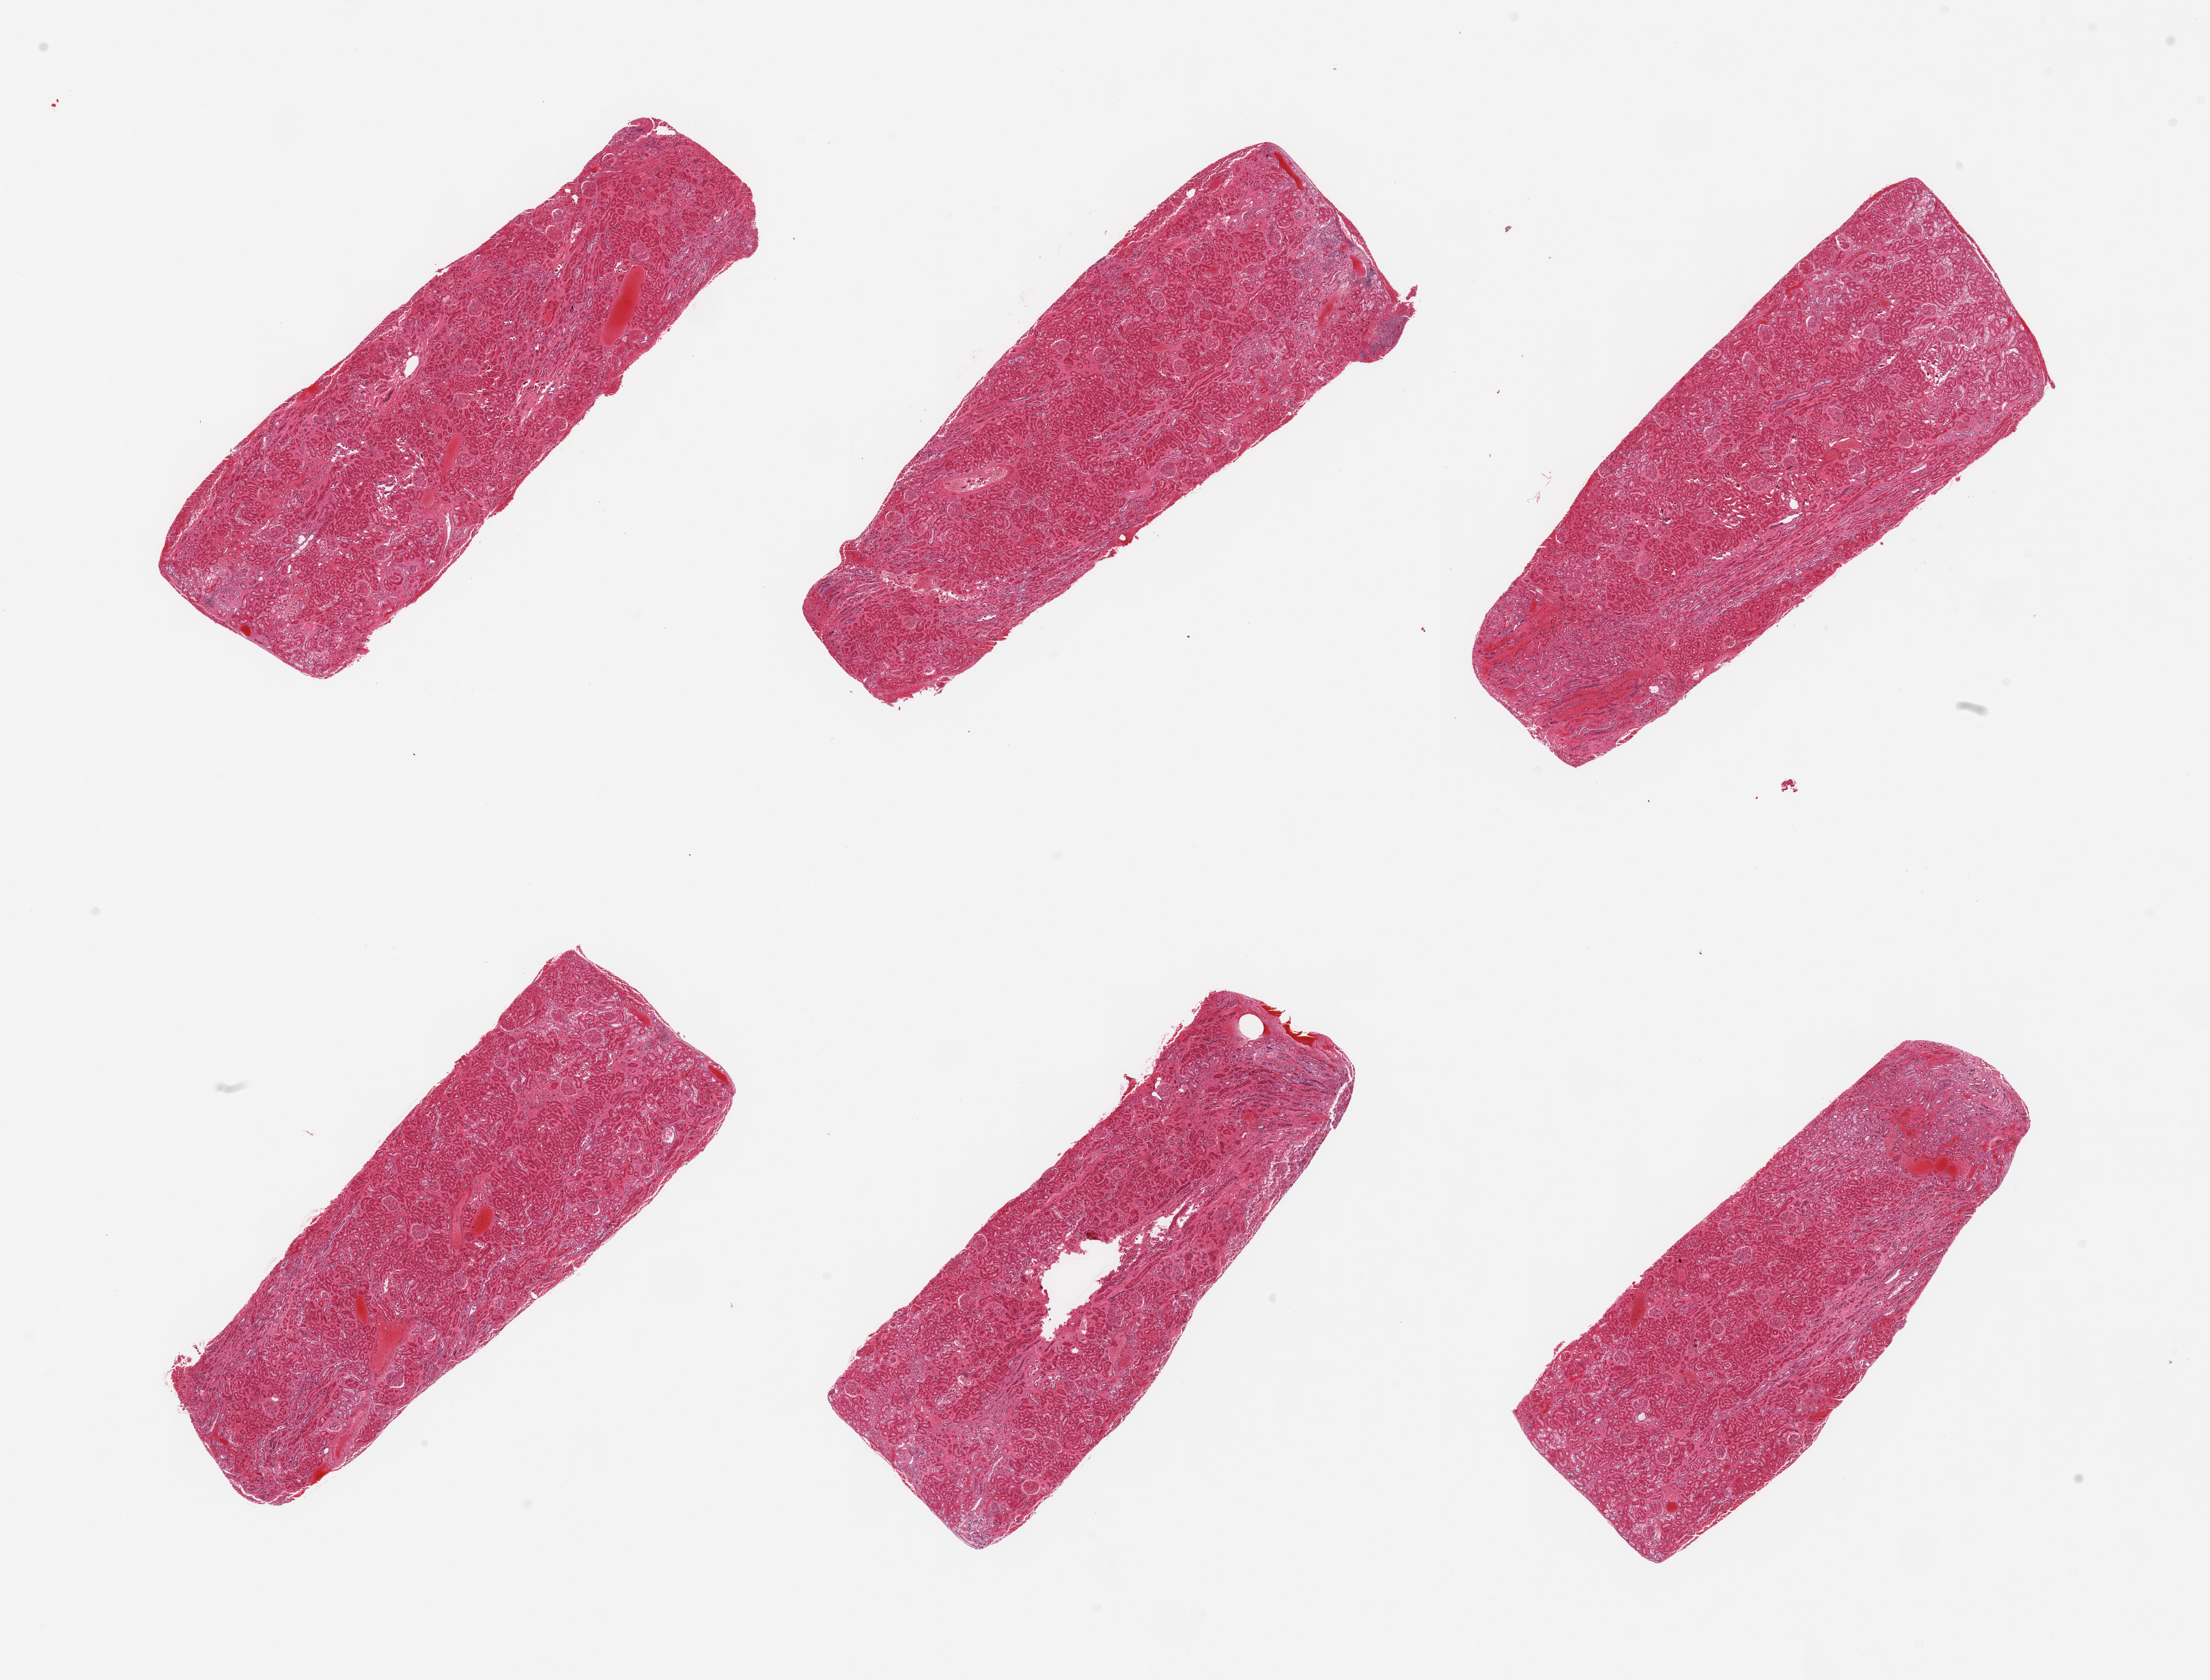
Whole-slide image, haematoxylin and eosin stain, brightfield, low-resolution overview of the scanned area, about 25.6 x 19.5 mm (acquisition: 20x scan), PAXgene-fixed paraffin-embedded (PFPE) section, target tissue: renal cortex, tissue donor sample.
Review note (as recorded): 6 pieces, glomeruli present.